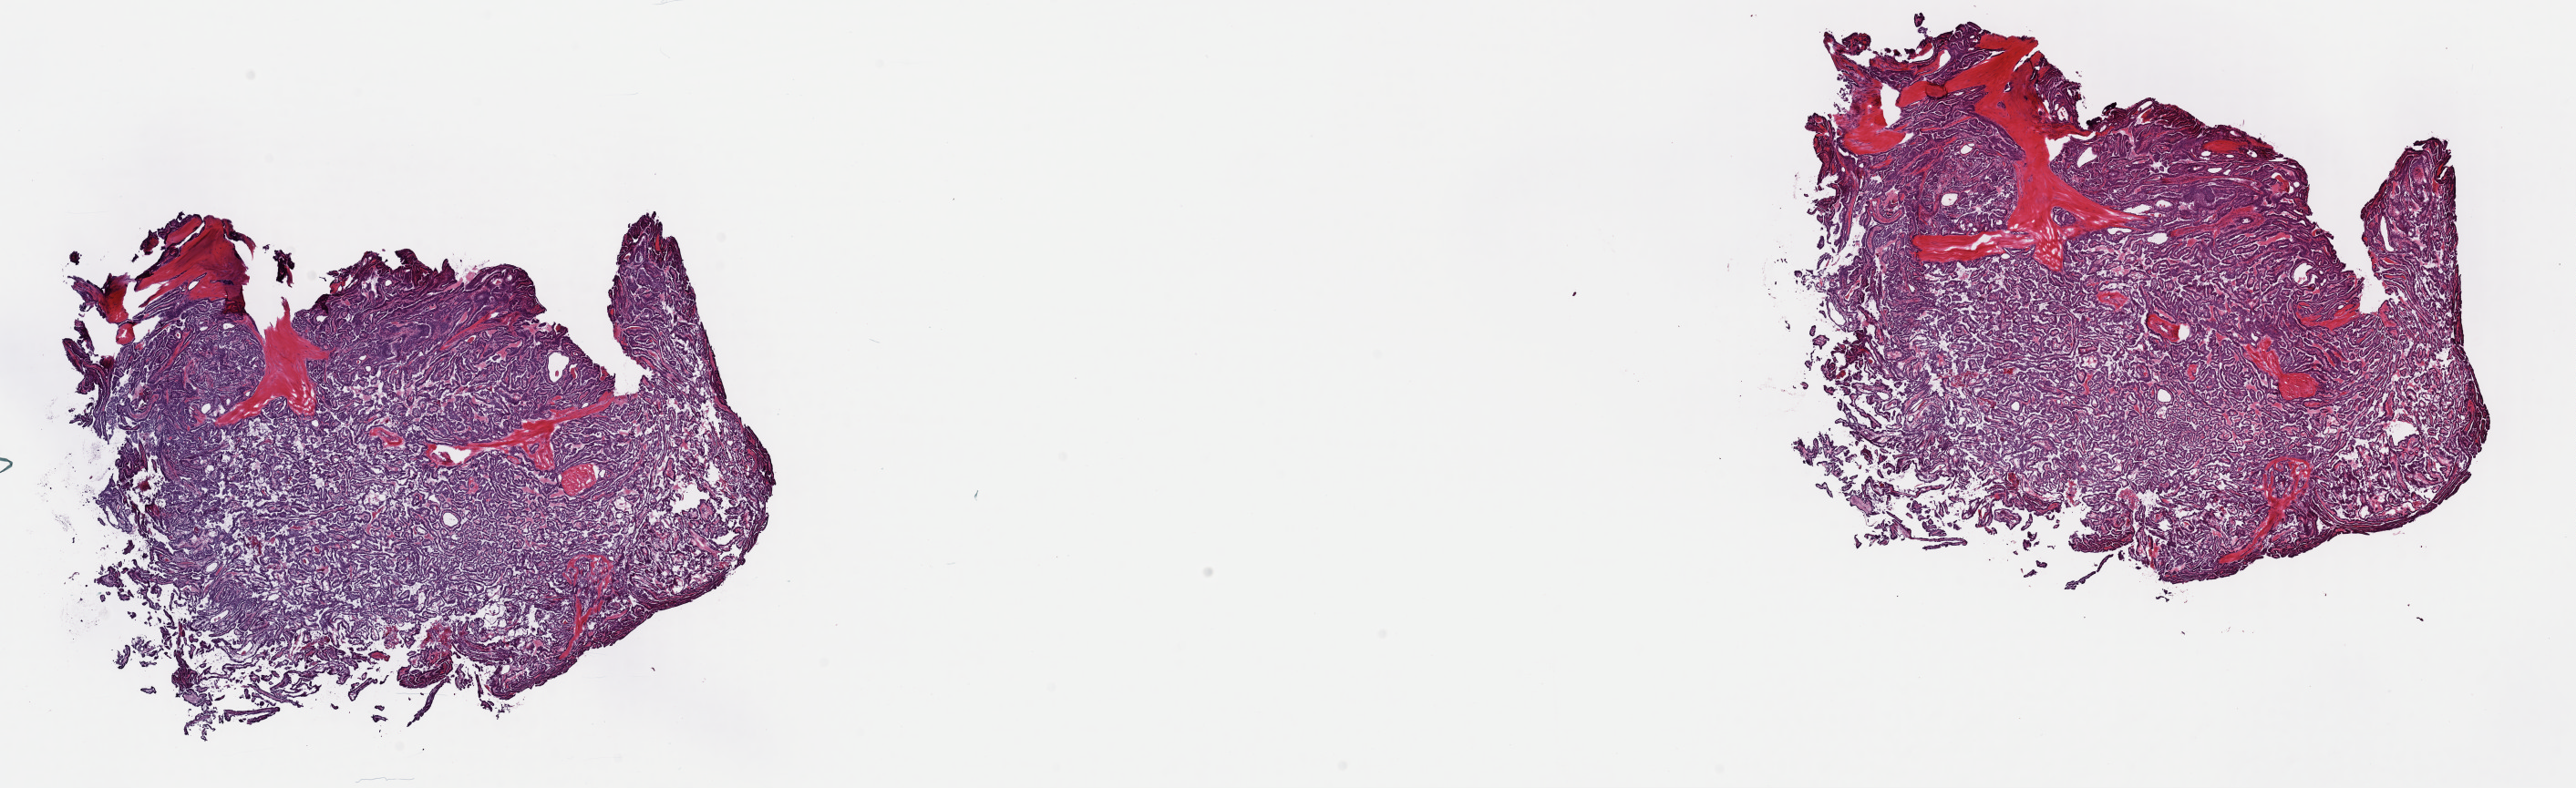
Whole-slide histology image, H&E — low-resolution overview of the scanned area, about 22.3 x 6.8 mm (acquisition: 40x scan), frozen section, thyroid, primary tumour sample. Female patient; age at initial diagnosis 52 years. Pathologist review of this section (percent, as recorded): tumour cells 85%, tumour nuclei 100%, normal cells 0%, stromal cells 15%, necrosis 0%. Inflammatory infiltration, as recorded: lymphocyte infiltration 2%, monocyte infiltration 1%, neutrophil infiltration 0%.
Diagnosis: Papillary adenocarcinoma, NOS (thyroid gland). Lymph nodes positive (case pathology): 2 of 9 examined. AJCC pathologic stage: III (7th edition).